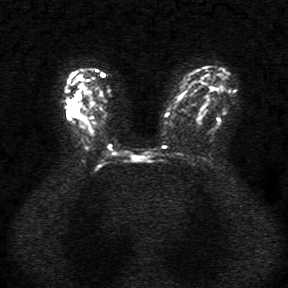
Breast MRI, one axial slice; position 21 of 34 along the scan axis; diffusion-weighted series; image 2 of 4 stored at this slice position (different b-values; order by instance number); 1.5 T; 5 mm slice thickness; 288 × 288 image matrix, field of view 340 × 340 mm. Female patient.
Outlined on this slice (expert manual segmentation):
- tumour on diffusion-weighted imaging: bounding box <74,95,80,108> (left, top, right, bottom; pixels)